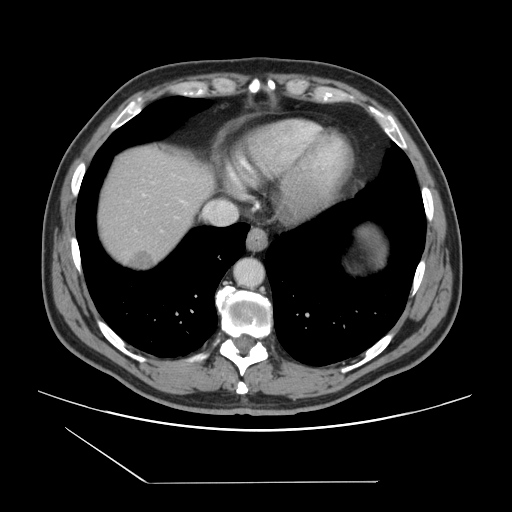
Contrast-enhanced abdominal CT, one axial slice. Position 132 of 157 along the scan axis. 120 kVp. Intravenous contrast given. Soft-tissue window (W 400 / L 40 HU). 2.5 mm slice thickness. 512 × 512 image matrix, field of view 407 × 407 mm. Male patient, age 61 years. From the clinical record (not read from this slice): diagnosis: colorectal cancer liver metastases, imaged before liver resection; multiple liver metastases: yes; largest metastasis: 5.5 cm; disease in both lobes: yes.
Annotated regions visible in this slice (manually delineated by an expert):
- liver: box from (x=97, y=148) to (x=211, y=270) px
- planned liver remnant (the part of the liver to remain after resection): (x=98, y=148)–(x=211, y=232)
- liver metastasis: (x=127, y=250)–(x=154, y=269)